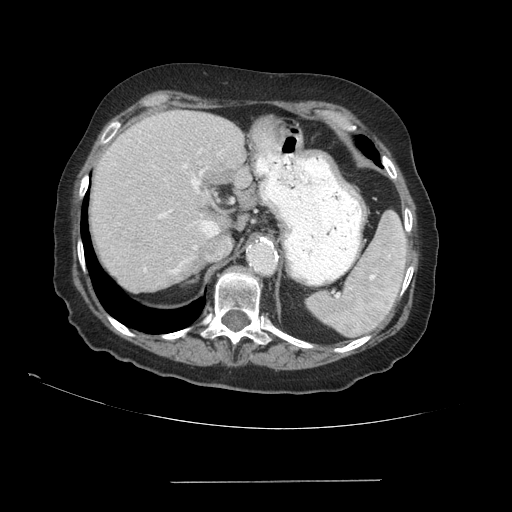
Contrast-enhanced abdominal CT (liver protocol), one axial slice. Slice 65 of 89 in the series (ordered by position). Reconstruction kernel STANDARD. 140 kVp. Soft-tissue window (W 400 / L 40 HU). 2.5 mm slice thickness. 512 × 512 image matrix, field of view 400 × 400 mm. From the clinical record (not read from this slice): diagnosis: hepatocellular carcinoma (patient treated with transarterial chemoembolisation; whether this scan precedes or follows treatment is not stated here); TNM stage (as recorded): Stage-IVA; Child-Pugh class: A.
Annotated regions visible in this slice (semi-automatic segmentation, software-assisted and operator-edited):
- liver parenchyma outside the tumour (the mass and vessels are separate outlines, so this box may not span the whole liver): bounding box [x1, y1, x2, y2] px = [90, 110, 250, 292]
- liver vessels: [144, 164, 207, 274]